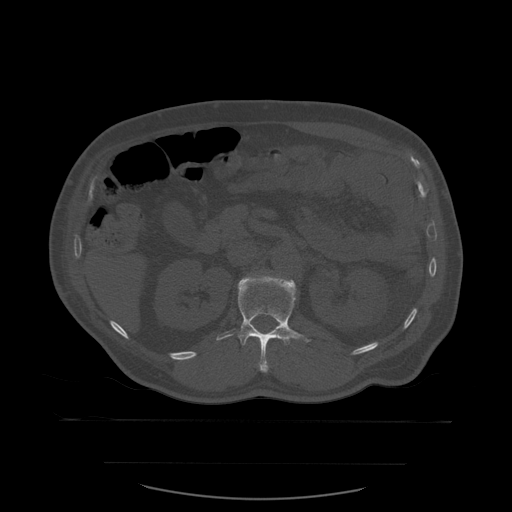
CT including the spine, one axial slice; position 246 of 590 along the scan axis; bone window (W 1800 / L 400 HU); 512 × 512 image matrix. Patient age 71 years. From the clinical record (not read from this slice): primary cancer: lung.
Outlined on this slice (semi-automatically segmented with operator editing):
- L1 vertebra: bounding box (x1, y1, x2, y2) in pixels: (216, 274, 312, 373)